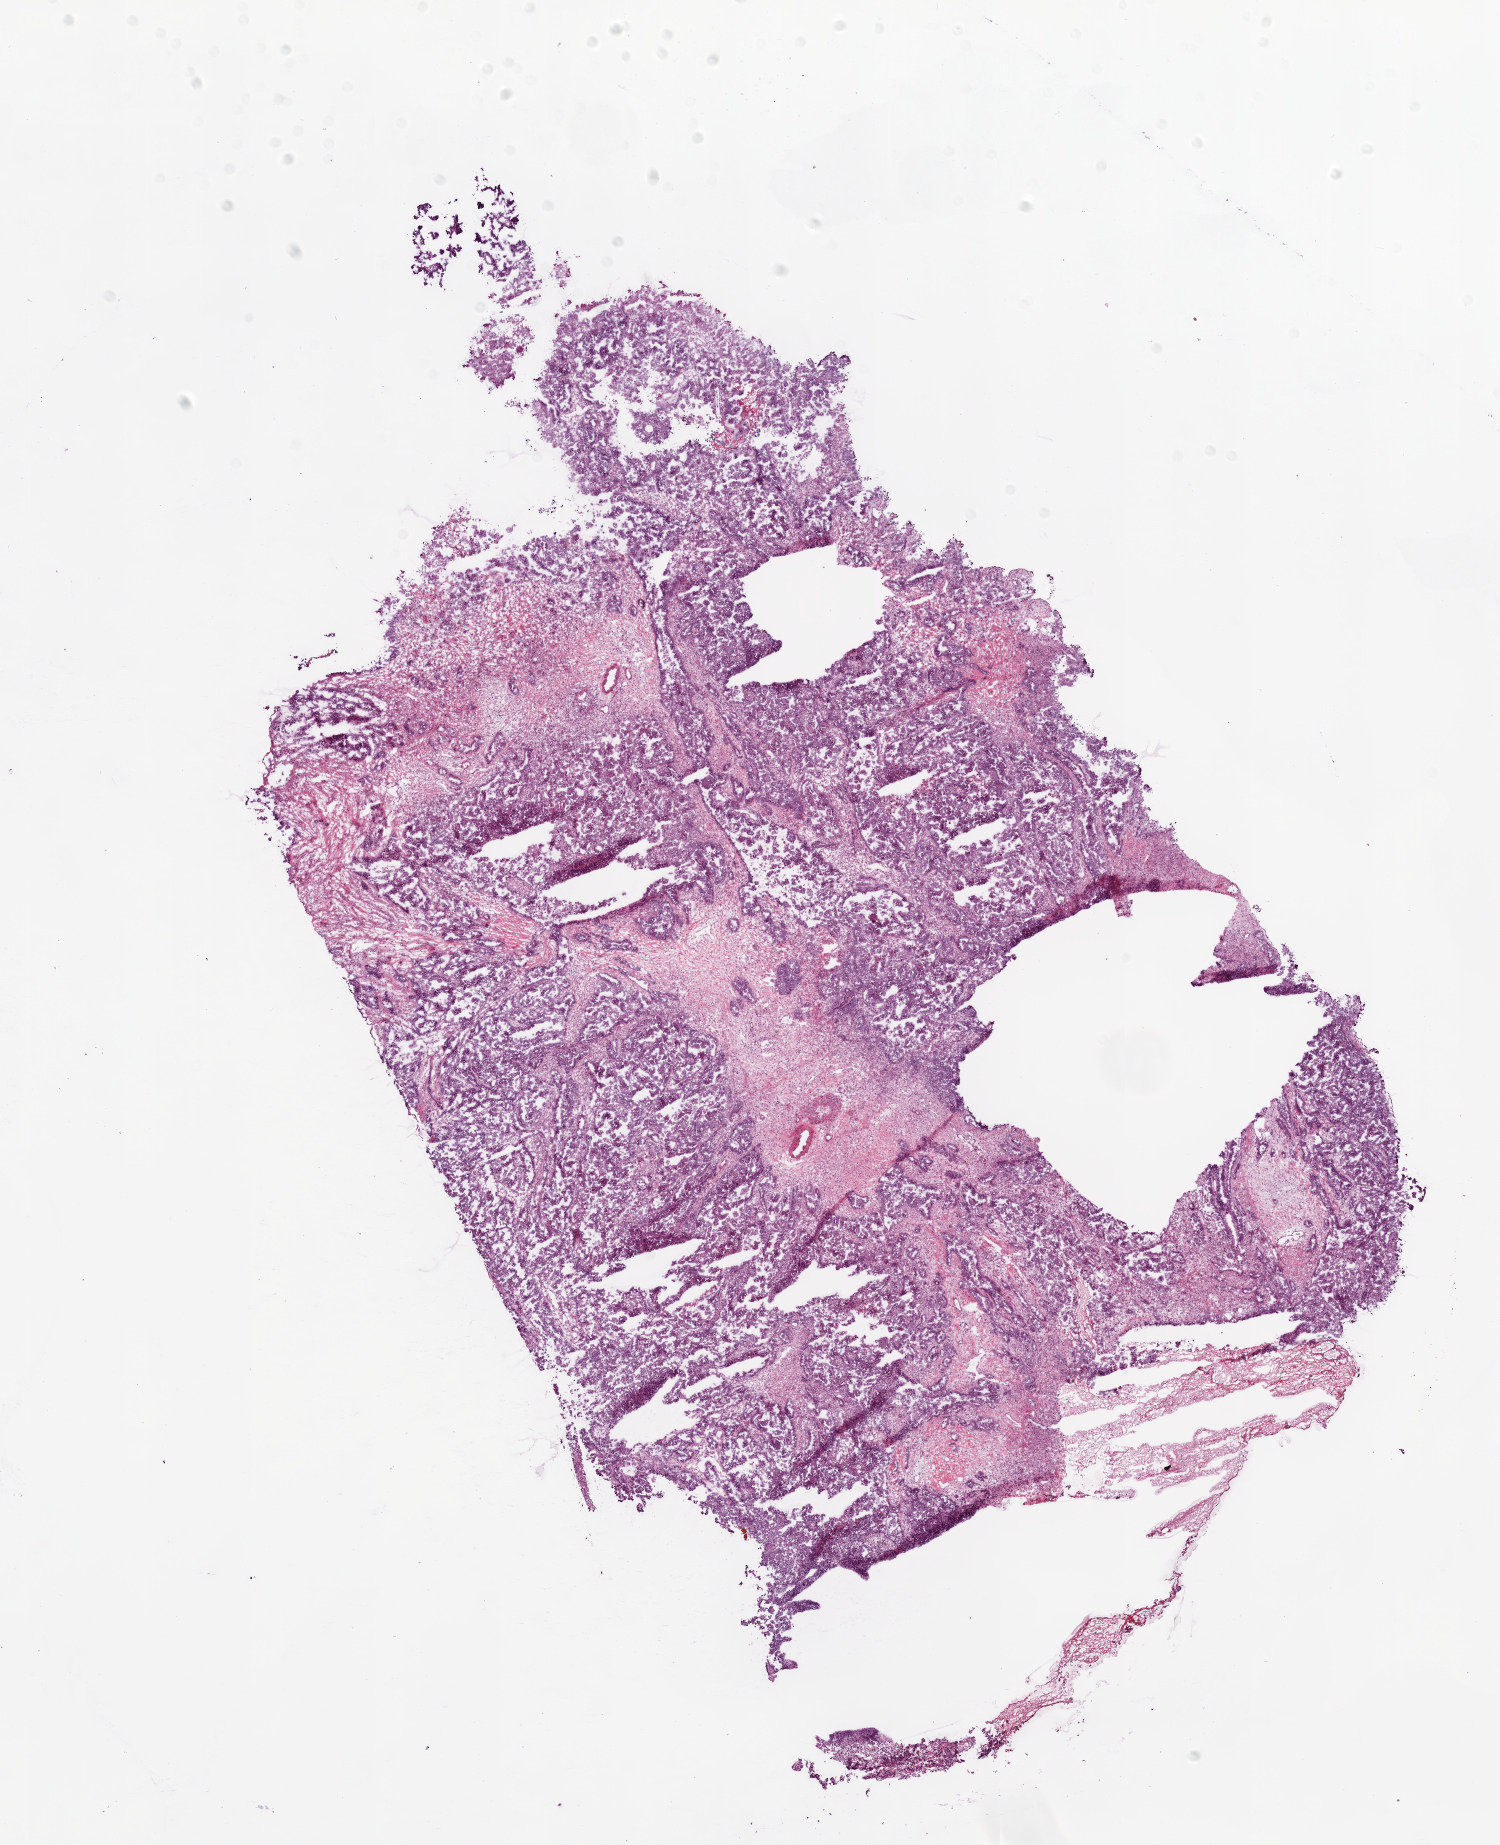
Digitized H&E tissue section (whole slide) — shown as a low-resolution overview of the whole scanned area (about 12.0 x 14.8 mm). Frozen section from the bottom of the tissue portion. Primary tumour sample from the ovary. Female patient; age at initial diagnosis 44 years. Histologic grade: G3 (poorly differentiated). Slide review estimates, as recorded: tumour cells 80%, tumour nuclei 90%, normal cells 0%, stromal cells 18%, necrosis 2%.
FIGO stage: IIIC. Diagnosis: Serous cystadenocarcinoma, NOS.